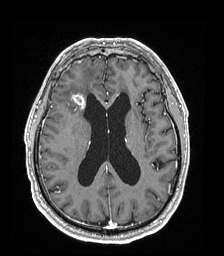
Brain MRI from a brain-tumour surgery series, one axial slice; position 82 of 192 along the scan axis; T1-weighted post-contrast; 1 mm slice thickness; 224 × 256 image matrix. From the clinical record (not read from this slice): histopathology: Astrocytoma; WHO grade: 4; IDH mutation: yes.
Structures marked on this image (manually delineated by an expert):
- tumour: box from (x=71, y=93) to (x=86, y=110) px